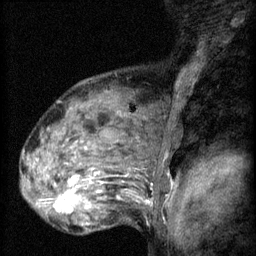
Breast MRI (dynamic contrast-enhanced), one sagittal slice; slice 43 of 60 in the series (ordered by position); 3 images stored at this slice position (order not interpretable as contrast timing); 1.5 T; TE 4.2 ms, TR 8.2 ms; 2 mm slice thickness; 256 × 256 image matrix, field of view 180 × 180 mm. Female patient, age 48 years.
Outlined on this slice (semi-automatic segmentation, software-assisted and operator-edited):
- analysis volume of interest (the breast-tissue region the enhancement analysis was run in; not a lesion): bounding box <48,160,125,217> (left, top, right, bottom; pixels)
- tumour enhancement mask (voxels above the 70 % enhancement threshold inside the analysis volume of interest): <53,178,119,213>